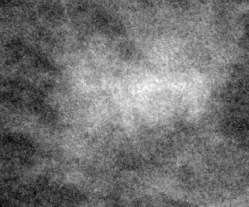
Region of interest cut from a scanned film mammogram (one marked finding); right breast; CC view; BI-RADS breast density category 1 (scale 1–4).
Finding: mass, shape irregular, margins ill defined; BI-RADS assessment category 4; subtlety rating 3 on a 1 (subtle) to 5 (obvious) scale; pathology result (as recorded, not read from the image): malignant.